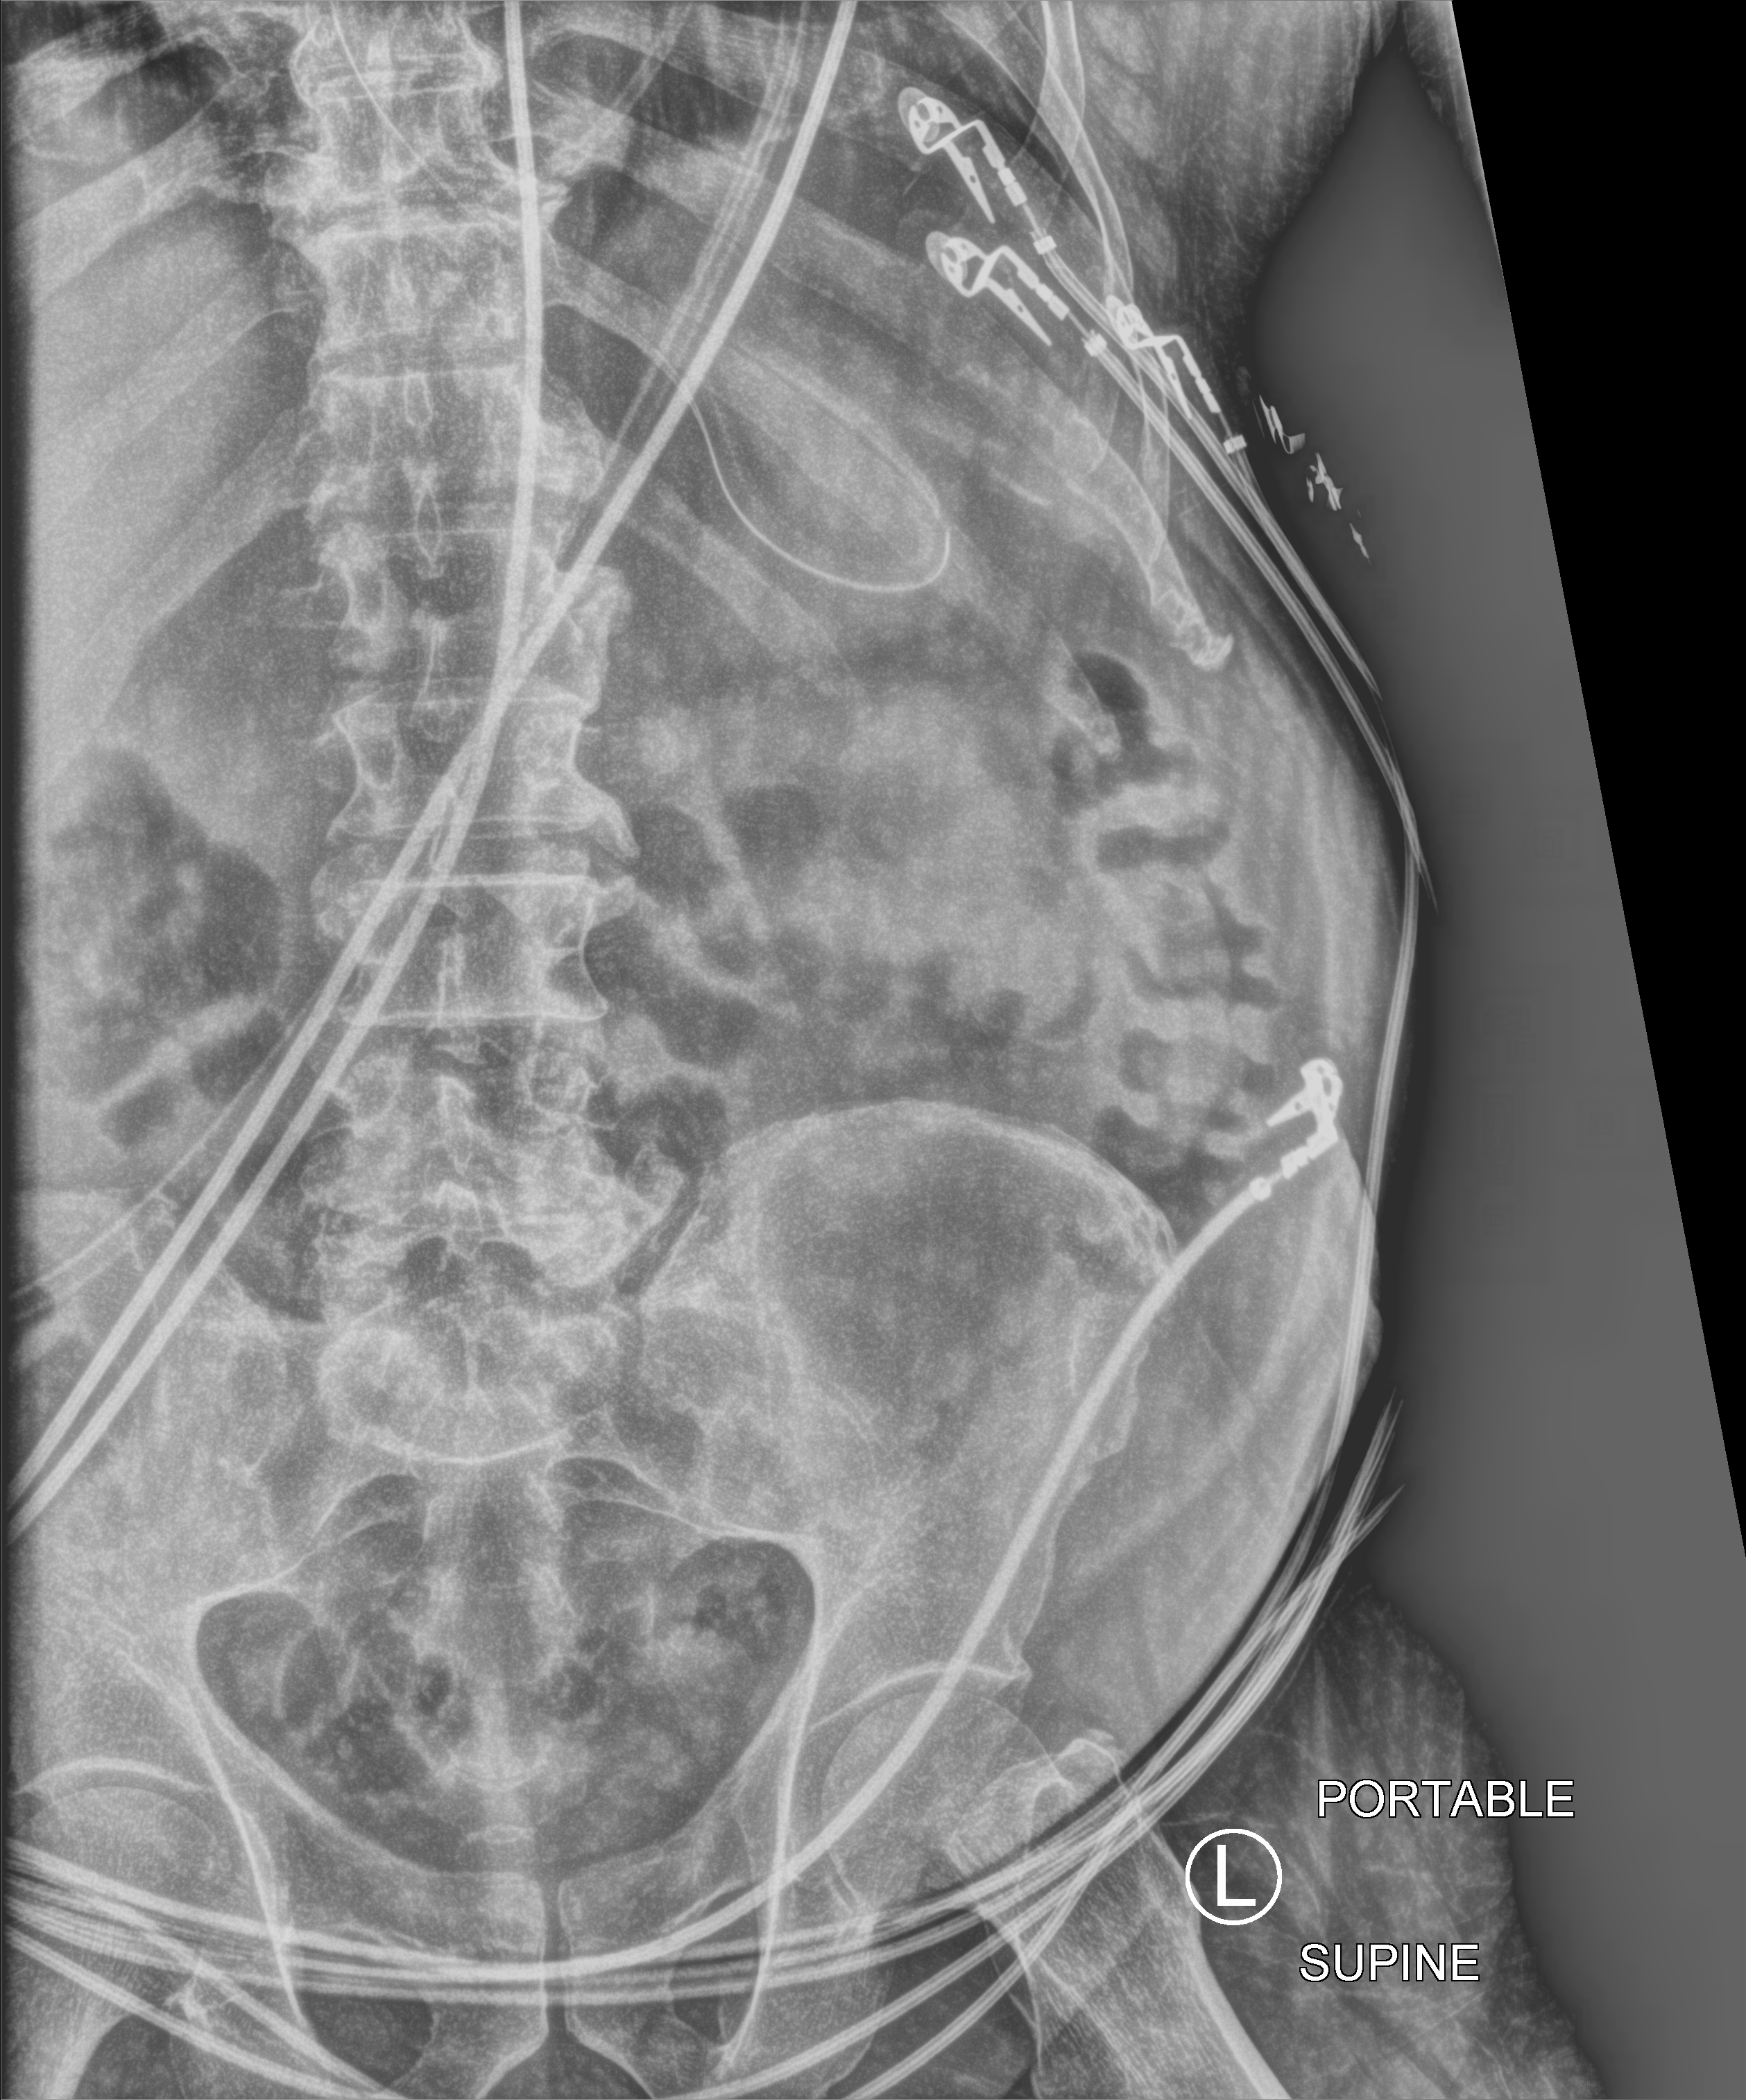
Portable abdomen radiograph. Patient hospitalised with COVID-19; male, aged 60–74 years.
Hospital-stay facts (about this admission, not read from this image; timing relative to this image not recorded): mechanically ventilated during this hospital stay: yes; diabetes (admission record): no; admitted to intensive care during this hospital stay: yes.